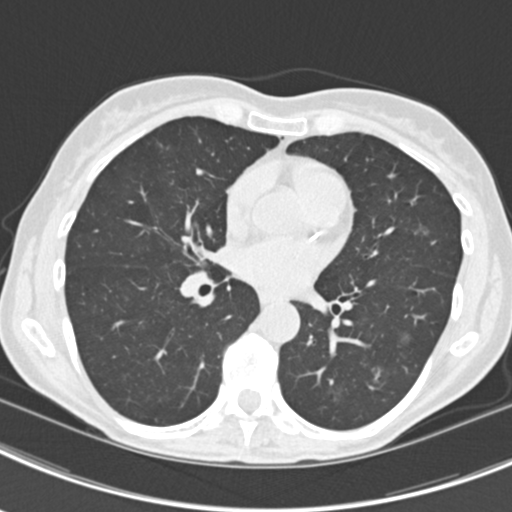
Low-dose screening chest CT, axial slice; second annual screen; lung window (W 1500 / L -600 HU); 2 mm slice thickness; standard (soft-tissue) reconstruction kernel (B30f); slice 99 of 219 in the series; 512 × 512 image matrix. Female, age 63 years at enrolment.
- Expert-annotated lung lesion, bounding box (x1, y1, x2, y2) in pixels: (396, 215, 435, 251).
- The screening reader recorded 9 non-calcified nodules or masses ≥4 mm on this exam (left upper lobe, right upper lobe, left upper lobe, left lower lobe, right middle lobe, left lower lobe, left lower lobe, right lower lobe, right lower lobe); which of them this box marks is not recorded.
- Official screen result: positive, other.
- Participant outcome: lung cancer diagnosed 408 days after this screen — bronchiolo-alveolar adenocarcinoma, NOS, right upper lobe, right middle lobe, right lower lobe, left upper lobe, left lower lobe, moderately differentiated (G2), stage IV (AJCC 6th edition).